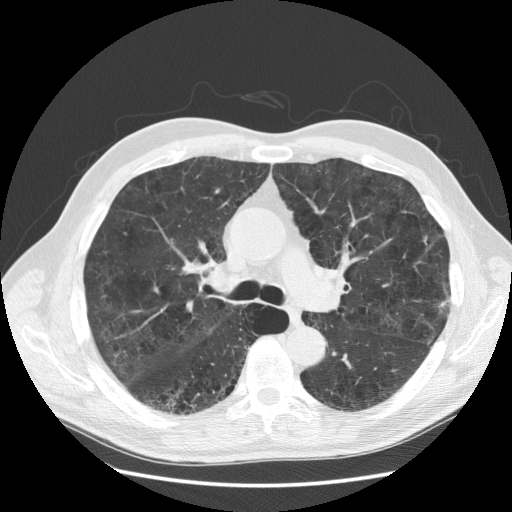
Low-dose screening chest CT, one axial slice. Position 97 of 163 along the scan axis. Reconstruction kernel STANDARD. 120 kVp. Lung window (W 1500 / L -600 HU). 512 × 512 image matrix, field of view 380 × 380 mm.
Structures marked on this image (outlined manually by an expert reader):
- lesion 1 (tumor, upper lobe of left lung): bounding box <424,234,433,247> (left, top, right, bottom; pixels)